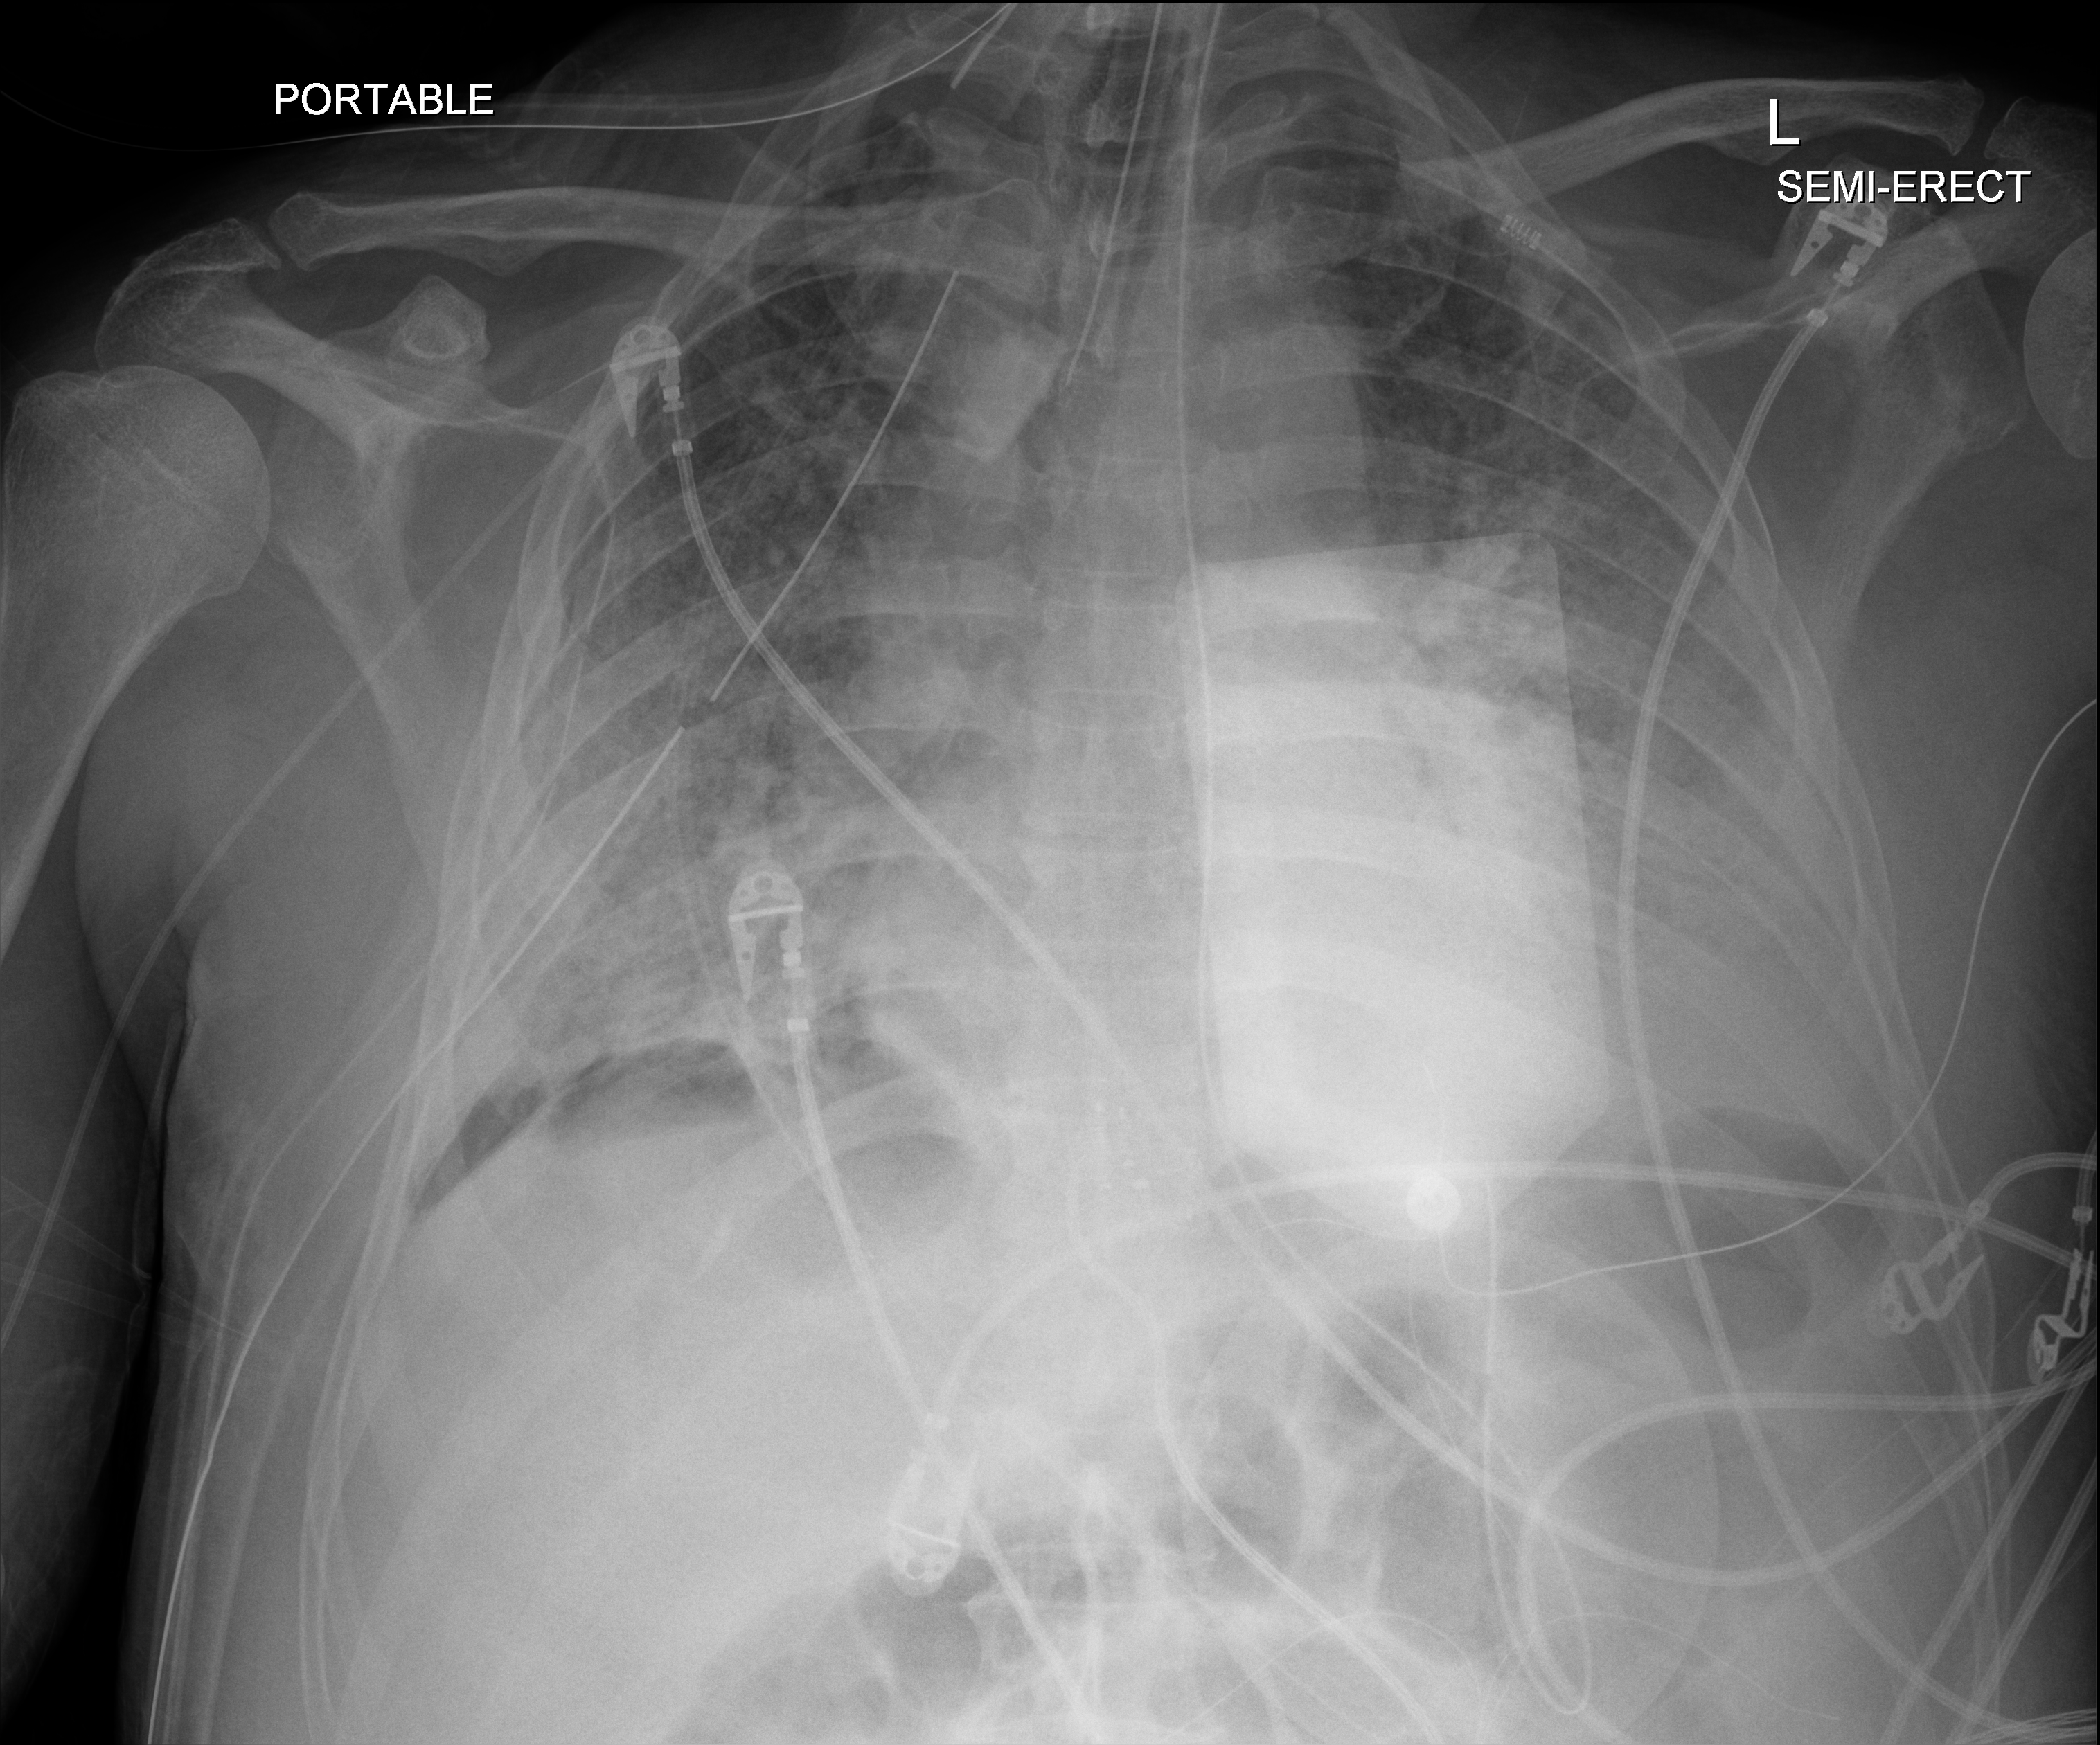
Chest X-ray (portable), anteroposterior (AP) projection. Patient hospitalised with COVID-19; male, aged 60–74 years.
Hospital-stay facts (about this admission, not read from this image; timing relative to this image not recorded): chronic kidney disease (admission record): no.